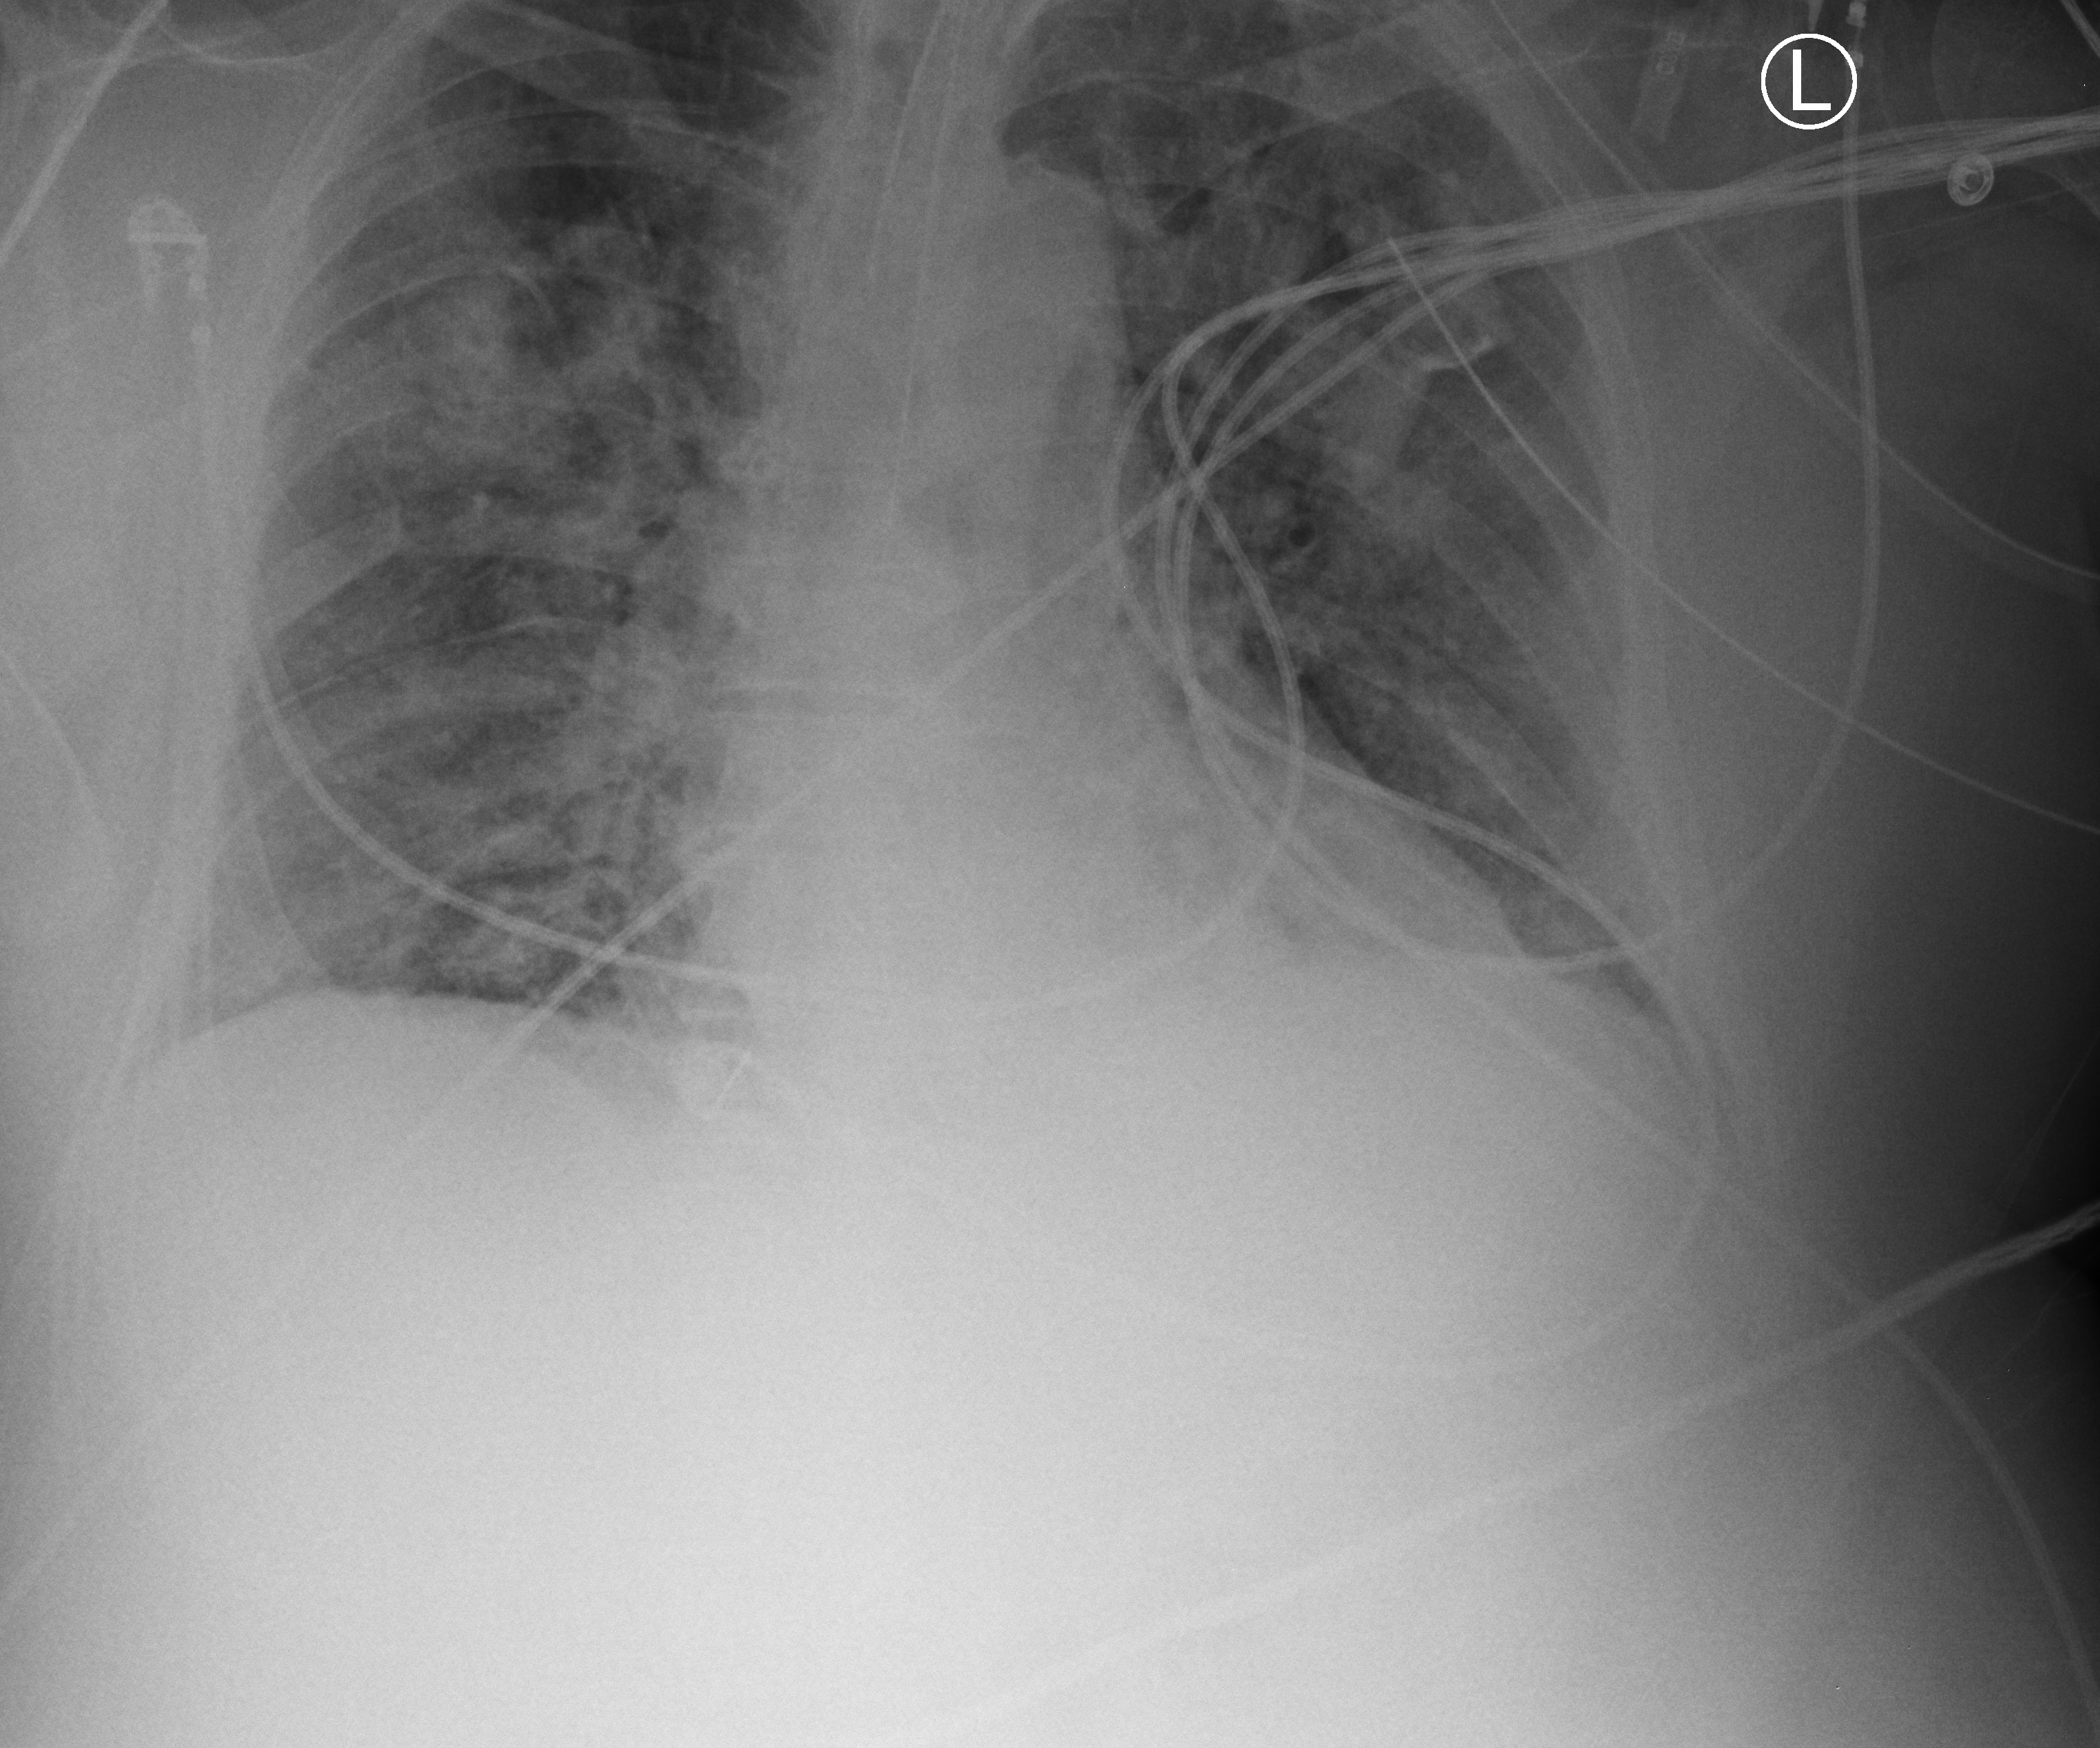
Chest X-ray (portable). Patient hospitalised with COVID-19; male, aged 60–74 years.
From the hospital-stay record, not from the radiograph (when in the stay this image was taken is not recorded):
- mechanically ventilated during this hospital stay: yes
- hypertension (admission record): yes